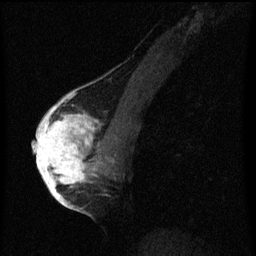
Breast MRI (dynamic contrast-enhanced), one sagittal slice; slice 31 of 60 in the series (ordered by position); dynamic contrast-enhanced series, image 2 of 3 at this slice position (ordered by acquisition); 1.5 T; TE 4.2 ms, TR 8 ms; 2 mm slice thickness; 256 × 256 image matrix, field of view 180 × 180 mm. Female patient, age 56 years.
Annotated regions visible in this slice (semi-automatically segmented with operator editing):
- analysis volume of interest (the breast-tissue region the enhancement analysis was run in; not a lesion): bounding box (x1, y1, x2, y2) in pixels: (42, 110, 105, 193)
- tumour enhancement mask (voxels above the 70 % enhancement threshold inside the analysis volume of interest): (42, 110, 99, 193)